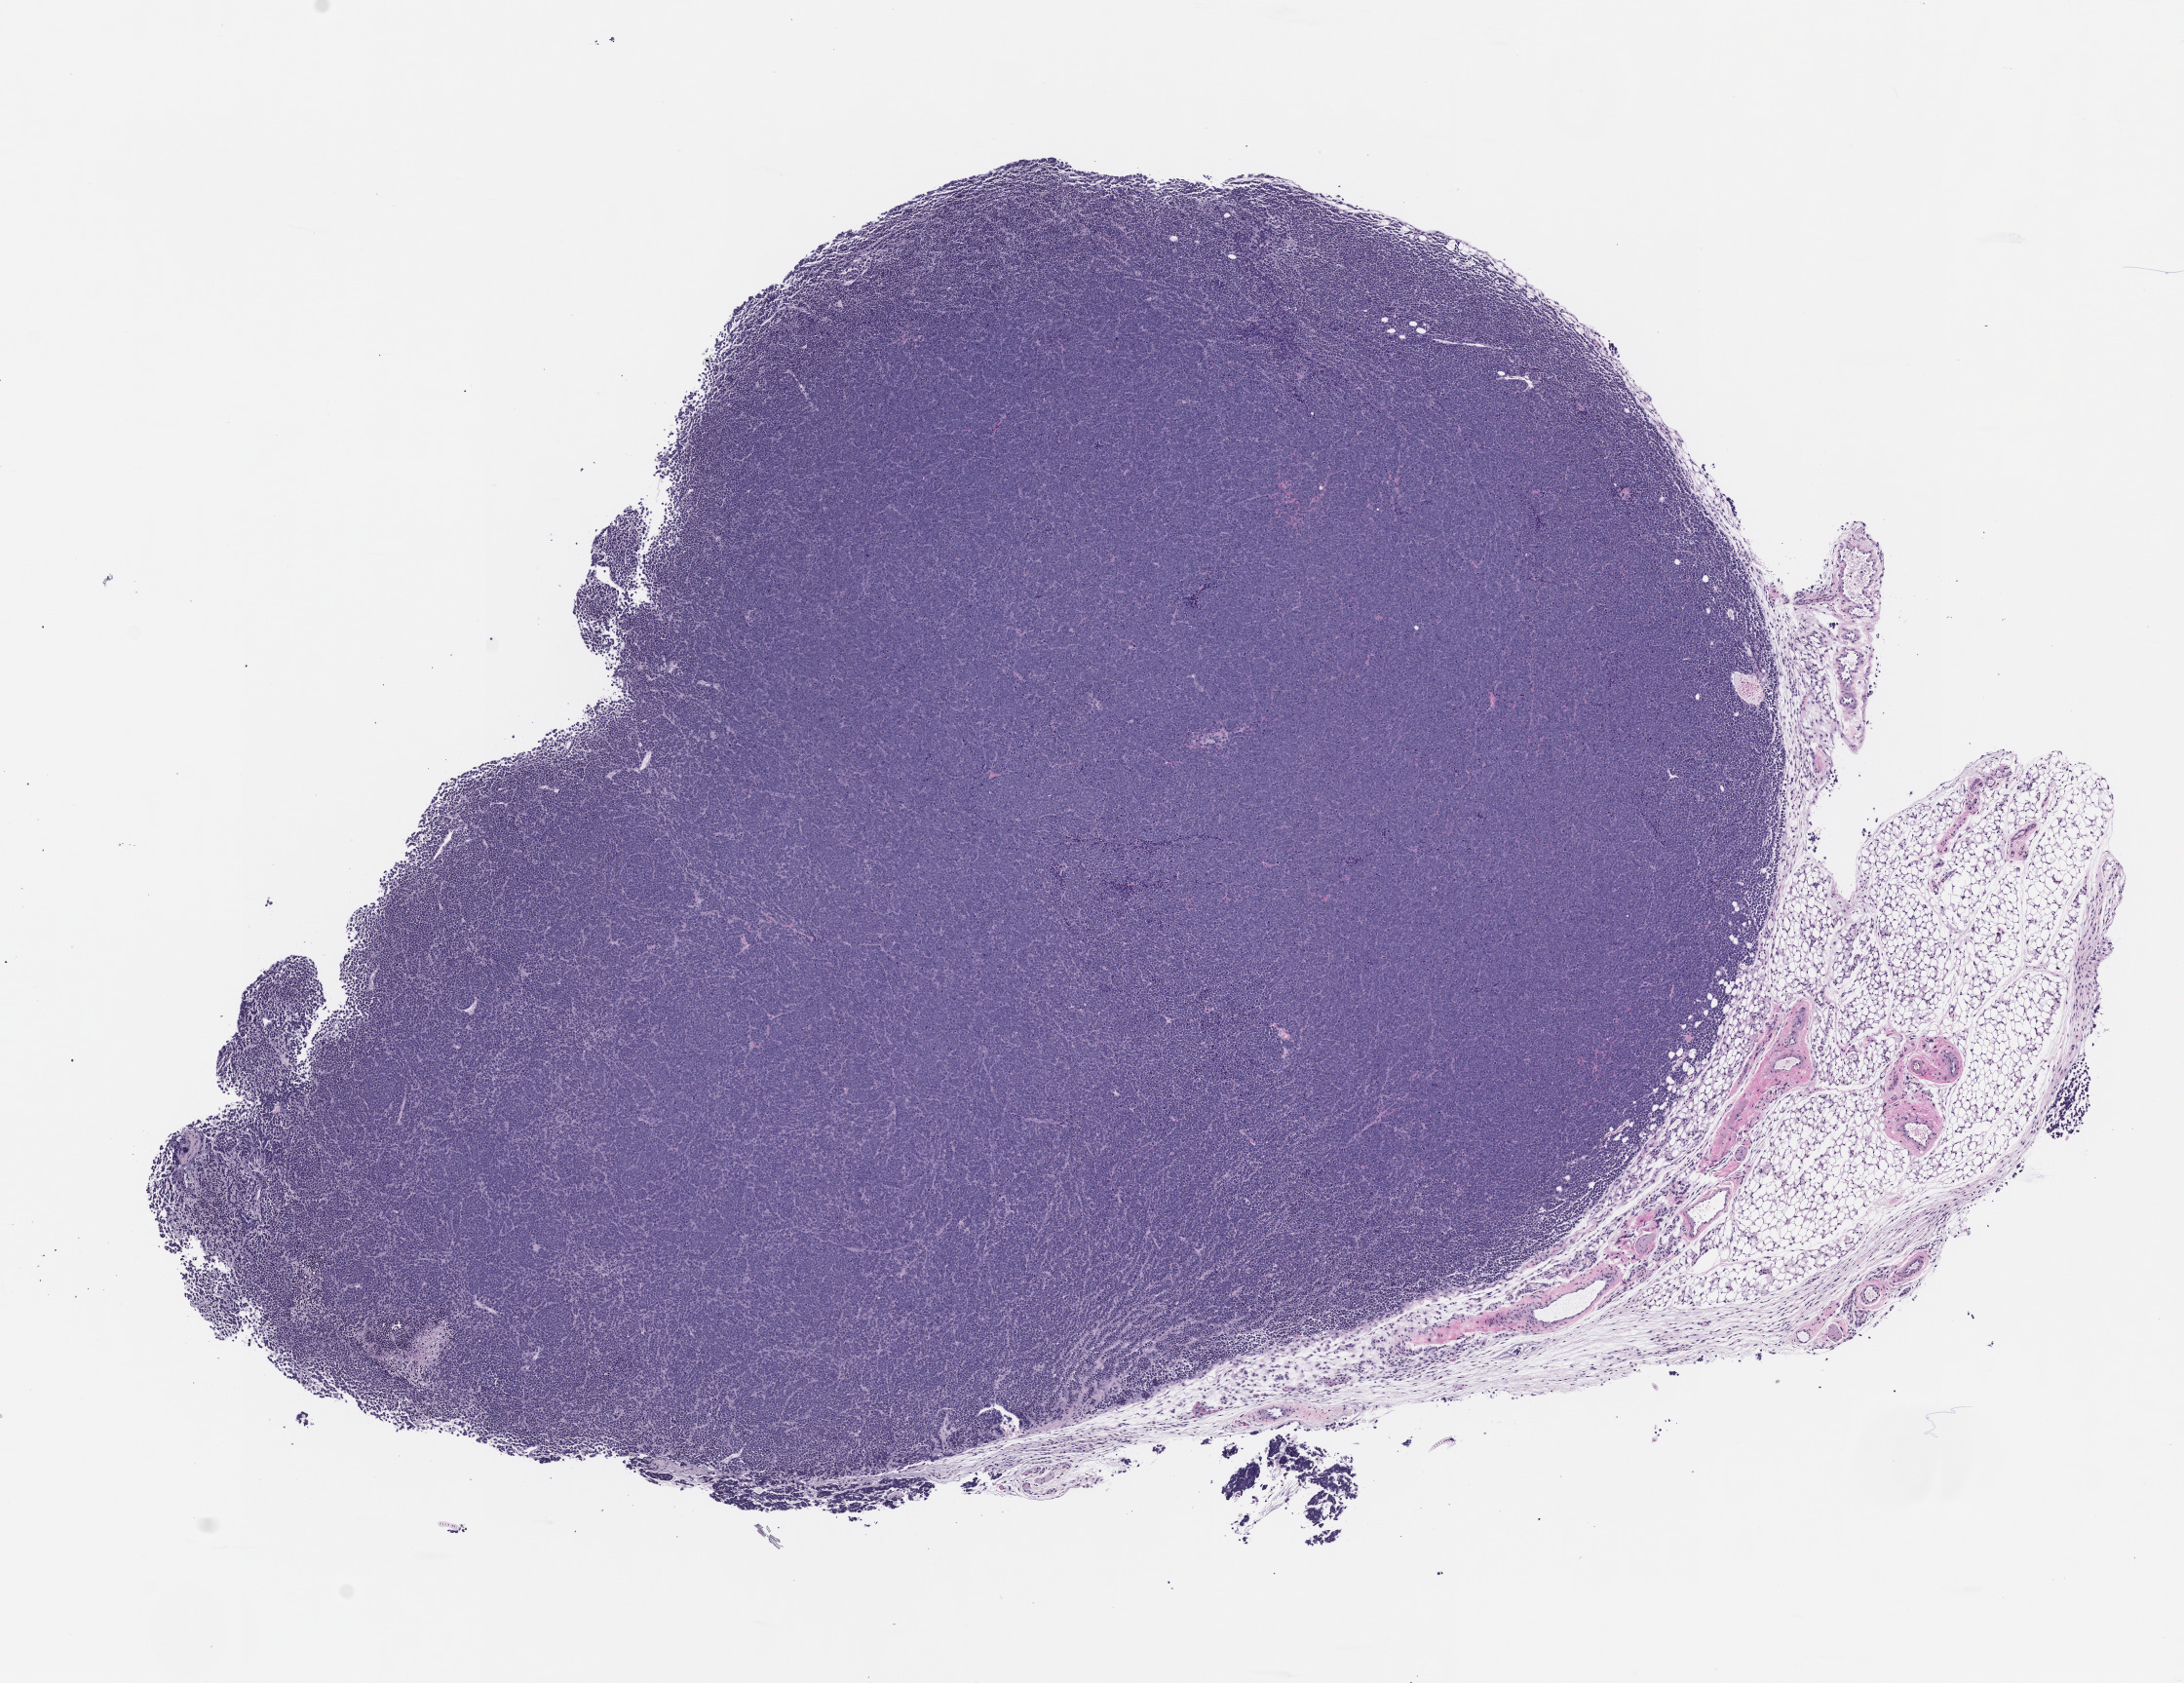
Haematoxylin and eosin whole-slide image of a patient-derived xenograft (PDX) tumor grown in a mouse, passage 3, a low-resolution overview of the entire scanned area, about 9.0 x 6.9 mm, formalin-fixed paraffin-embedded section, originating tumor site category: endocrine.
Originating patient diagnosis: Merkel Cell Carcinoma.